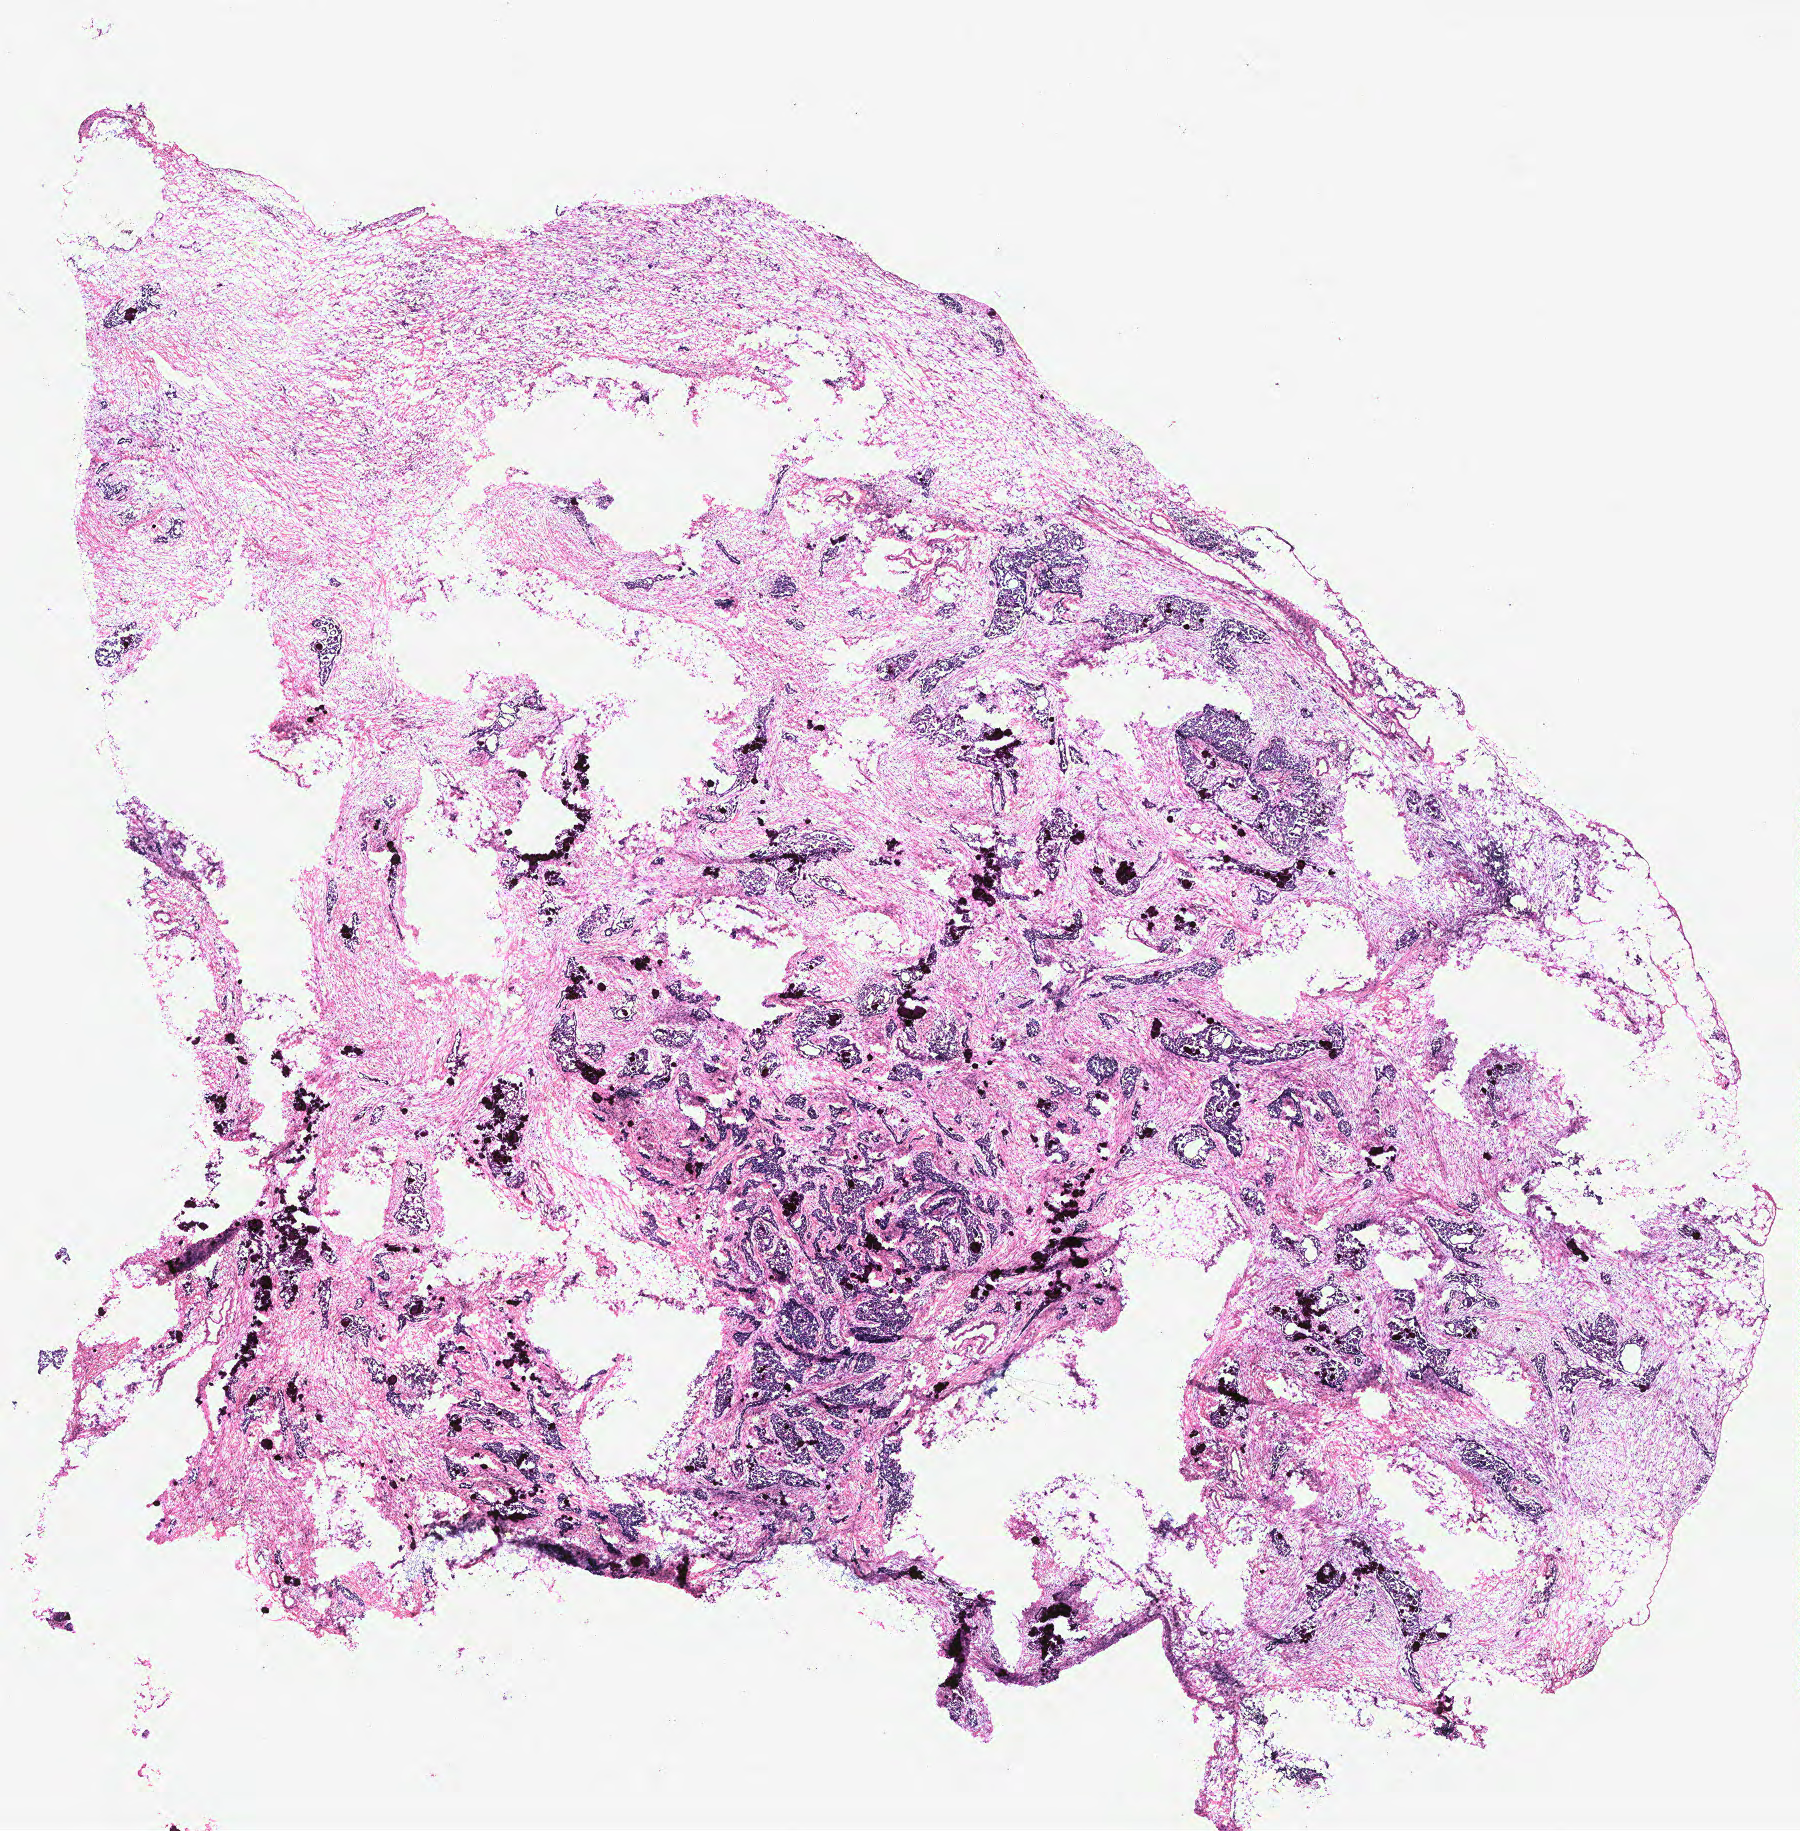
H&E-stained whole-slide image — whole scanned area (about 14.4 x 14.7 mm) shown as a low-resolution overview; ovary, tumour tissue. Patient: female, age 63 years.
* primary tumour site (as recorded): ovary
* histologic diagnosis: Serous adenocarcinoma, NOS